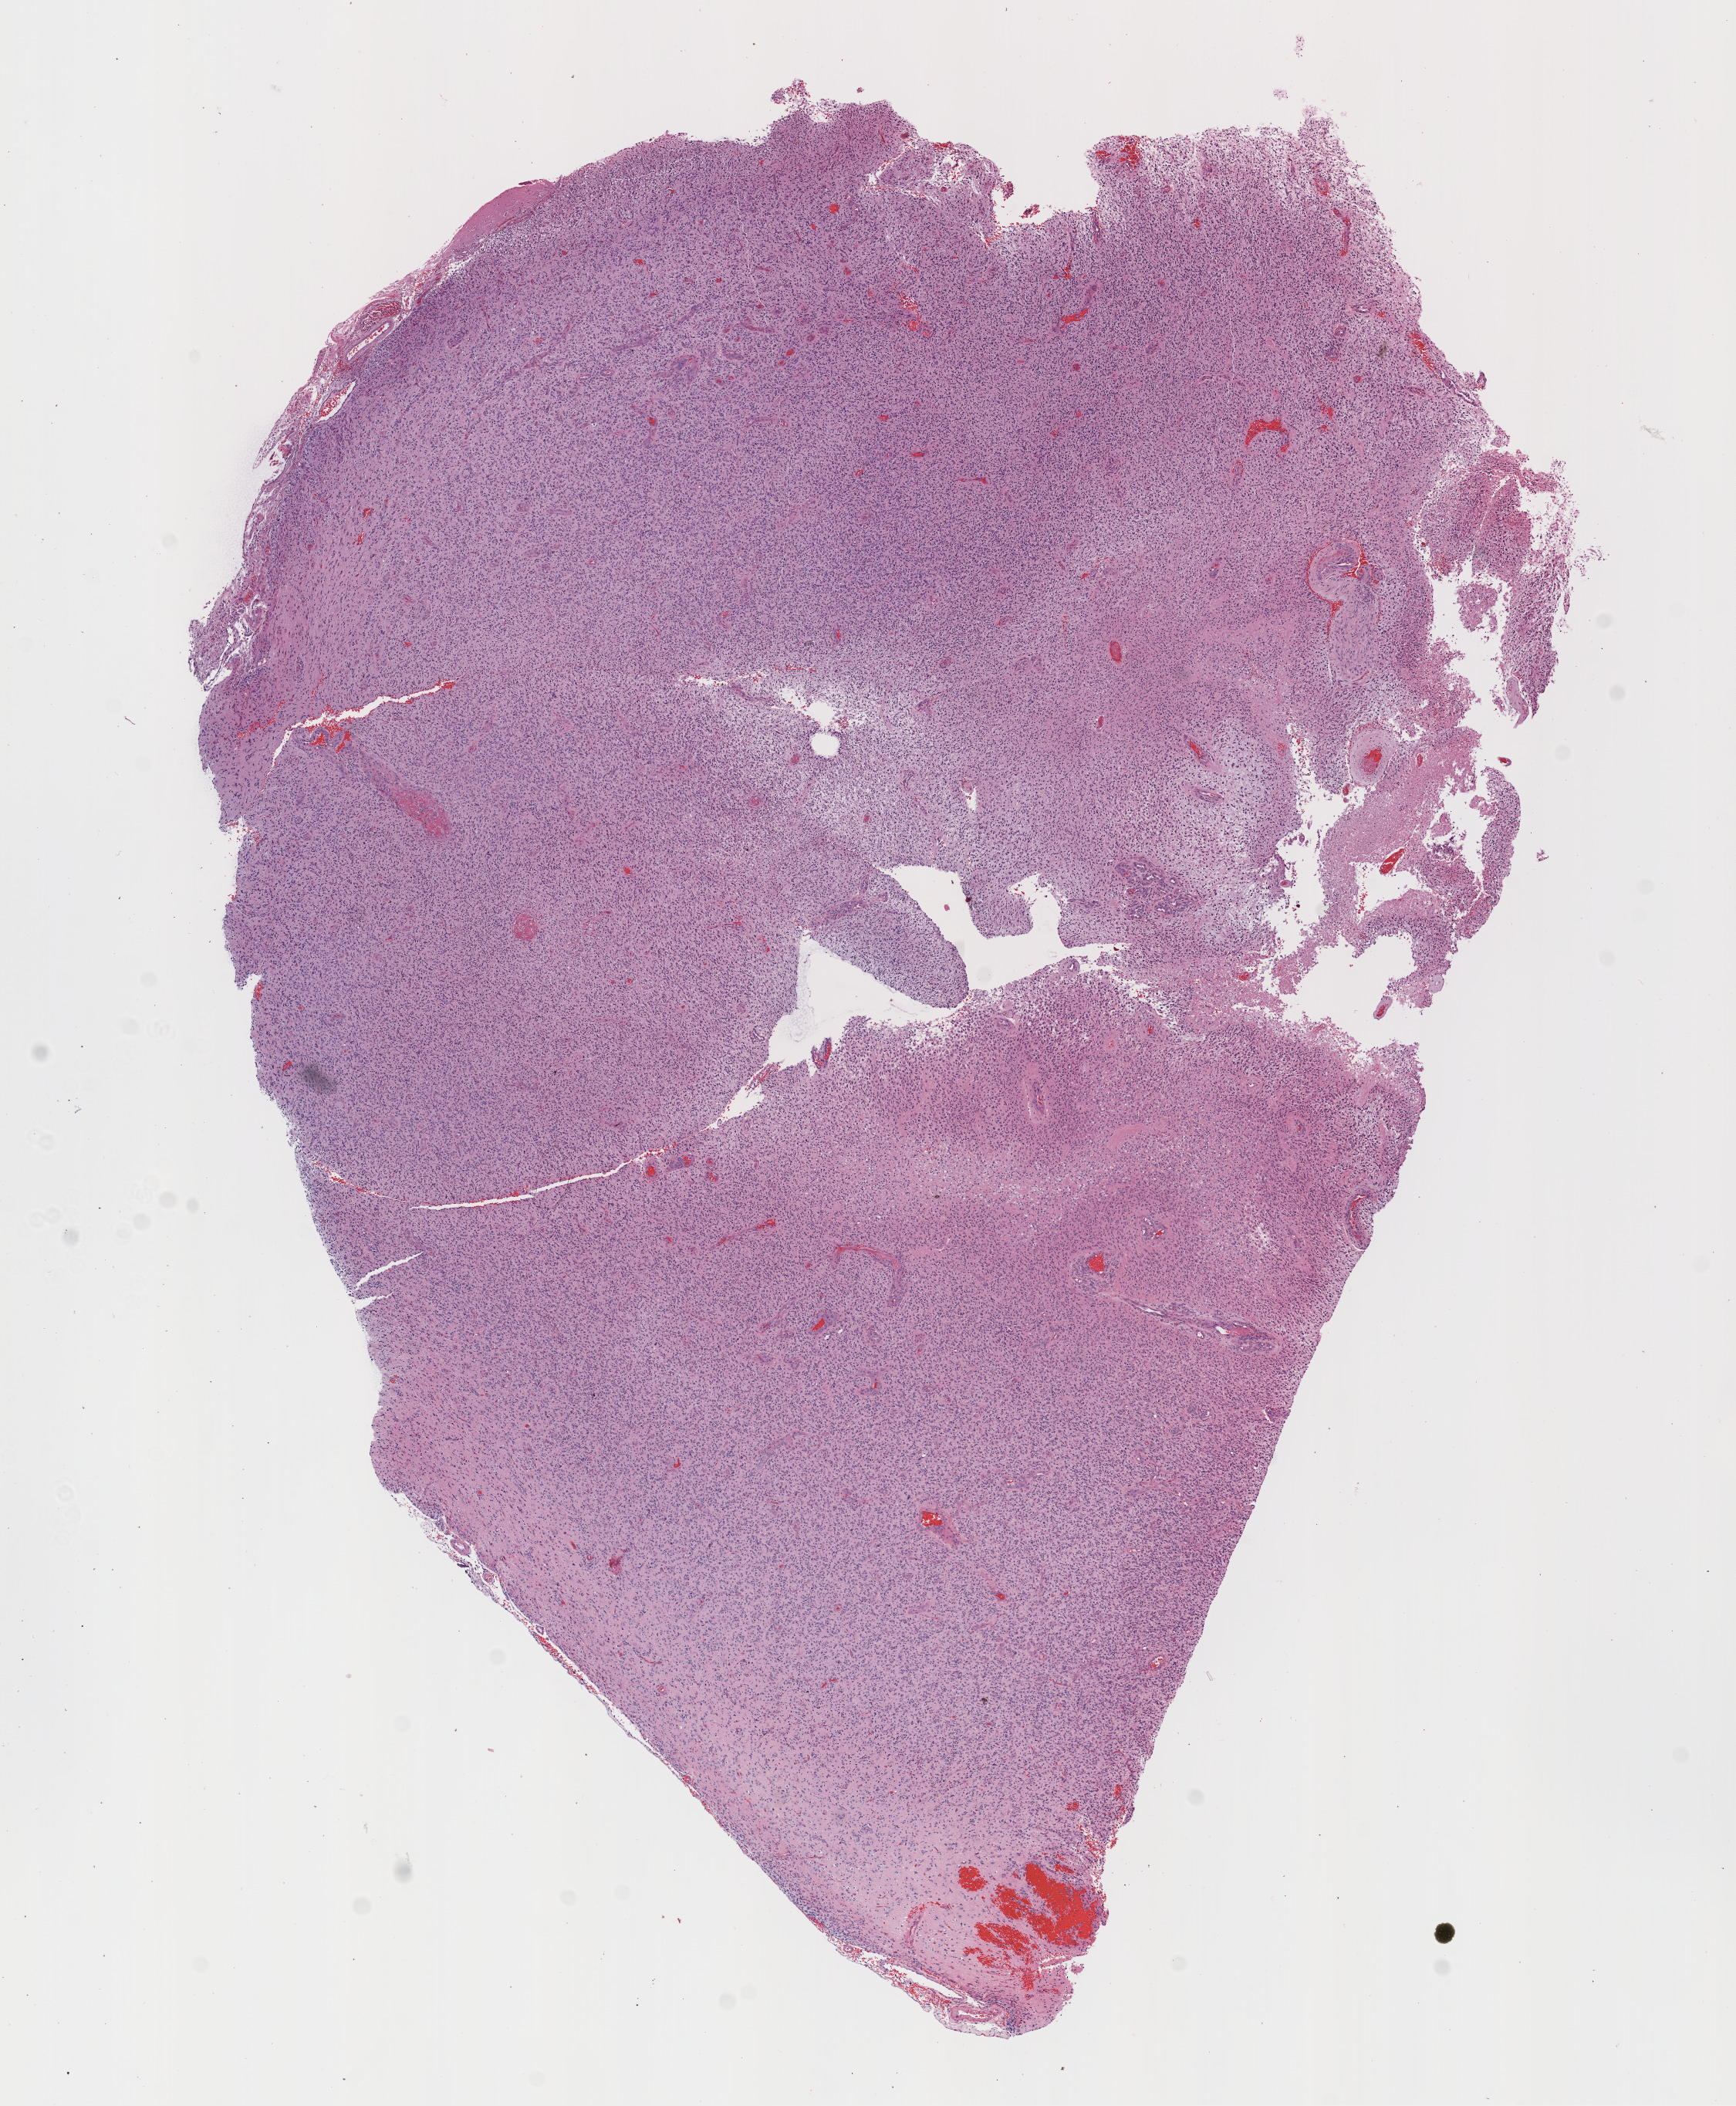
Digitized H&E tissue section (whole slide), shown as a low-resolution overview of the whole scanned area (about 9.0 x 10.9 mm, acquisition: 20x scan), FFPE section, brain, primary tumour sample. Patient: female, age at initial diagnosis 84 years.
• pathologic diagnosis: Glioblastoma